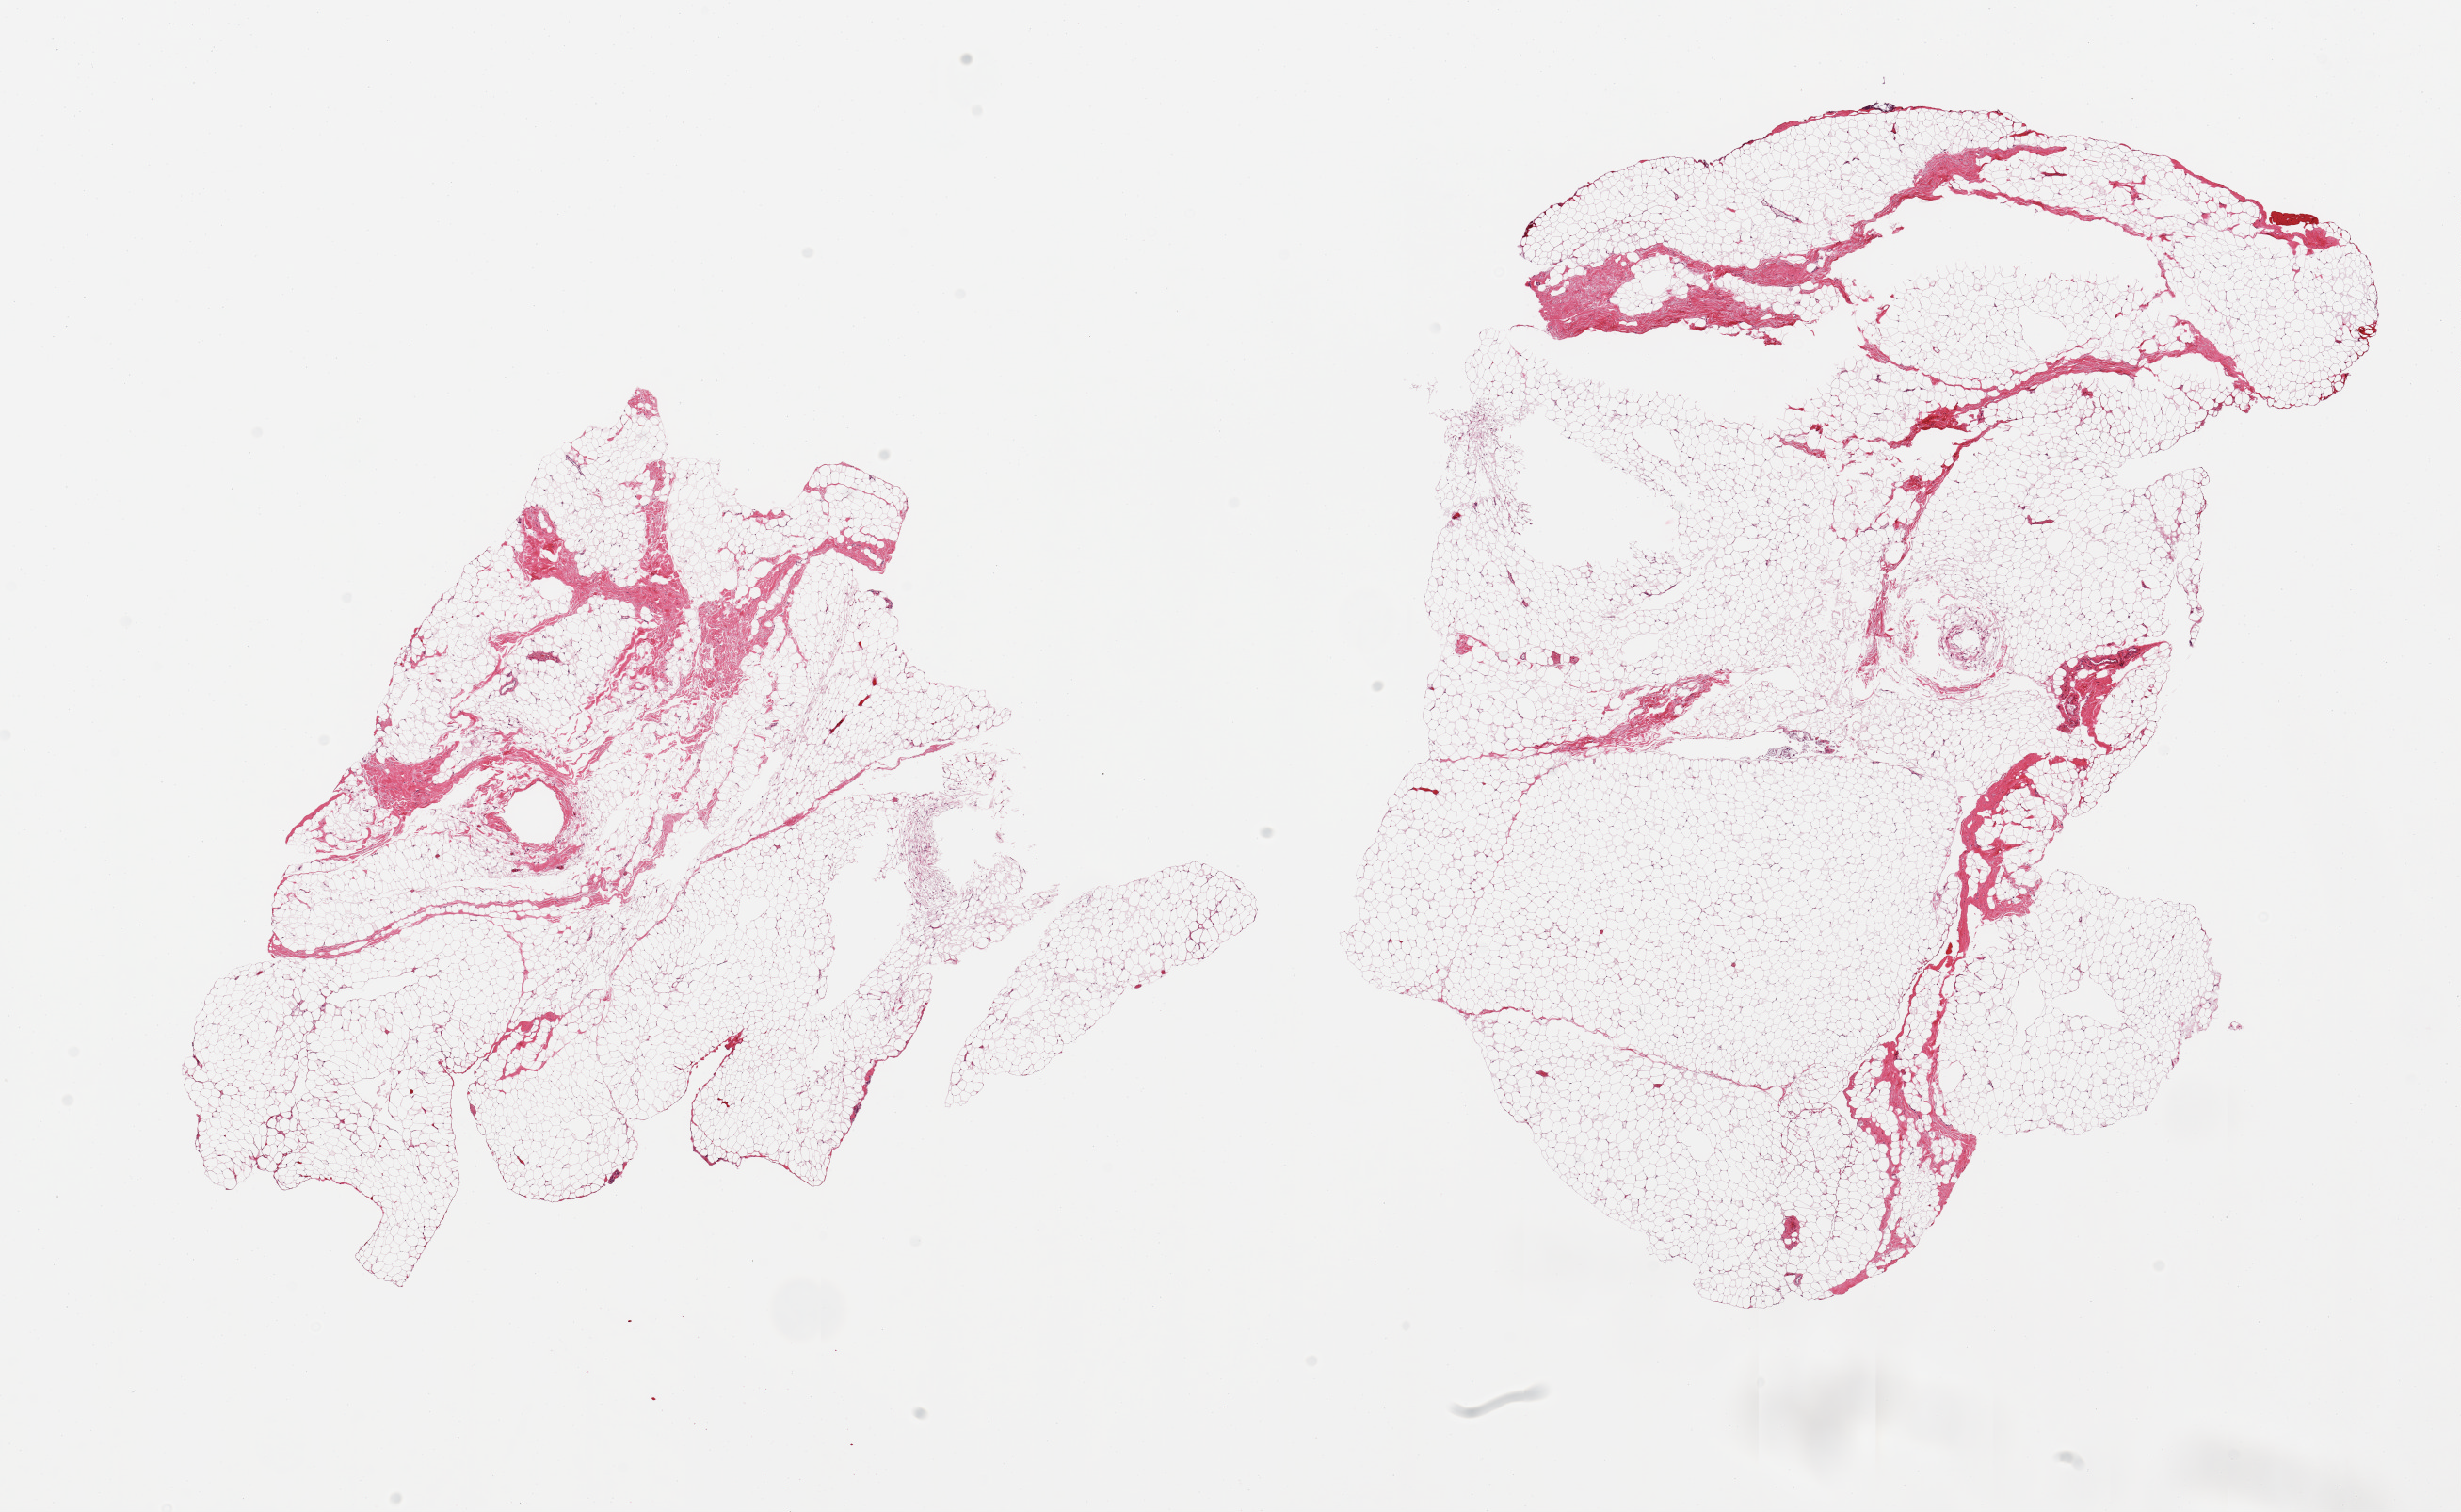
Digitized H&E-stained section, brightfield — low-resolution overview of the scanned area, about 20.7 x 12.7 mm, PAXgene-fixed, paraffin-embedded tissue, target tissue: breast, tissue donor sample.
* review note (as recorded): 2 pieces; mainly adipose tissue and ~ 10% fibrovascular component, no ductal elements identified, detached fragment of skeletal muscle